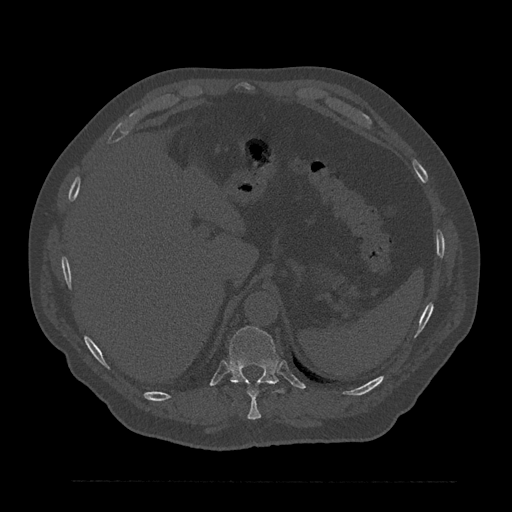
CT including the spine, one axial slice. Reconstruction kernel Br40s/3. 120 kVp. Bone window (W 1800 / L 400 HU). 0.5 mm slice thickness. 512 × 512 image matrix. Male patient, age 61 years. Case-level facts recorded for this patient, not image findings: primary cancer: prostate.
Structures marked on this image (semi-automatically segmented with operator editing):
- T10 vertebra: box from (x=233, y=382) to (x=261, y=420) px
- T11 vertebra: (x=229, y=326)–(x=285, y=393)